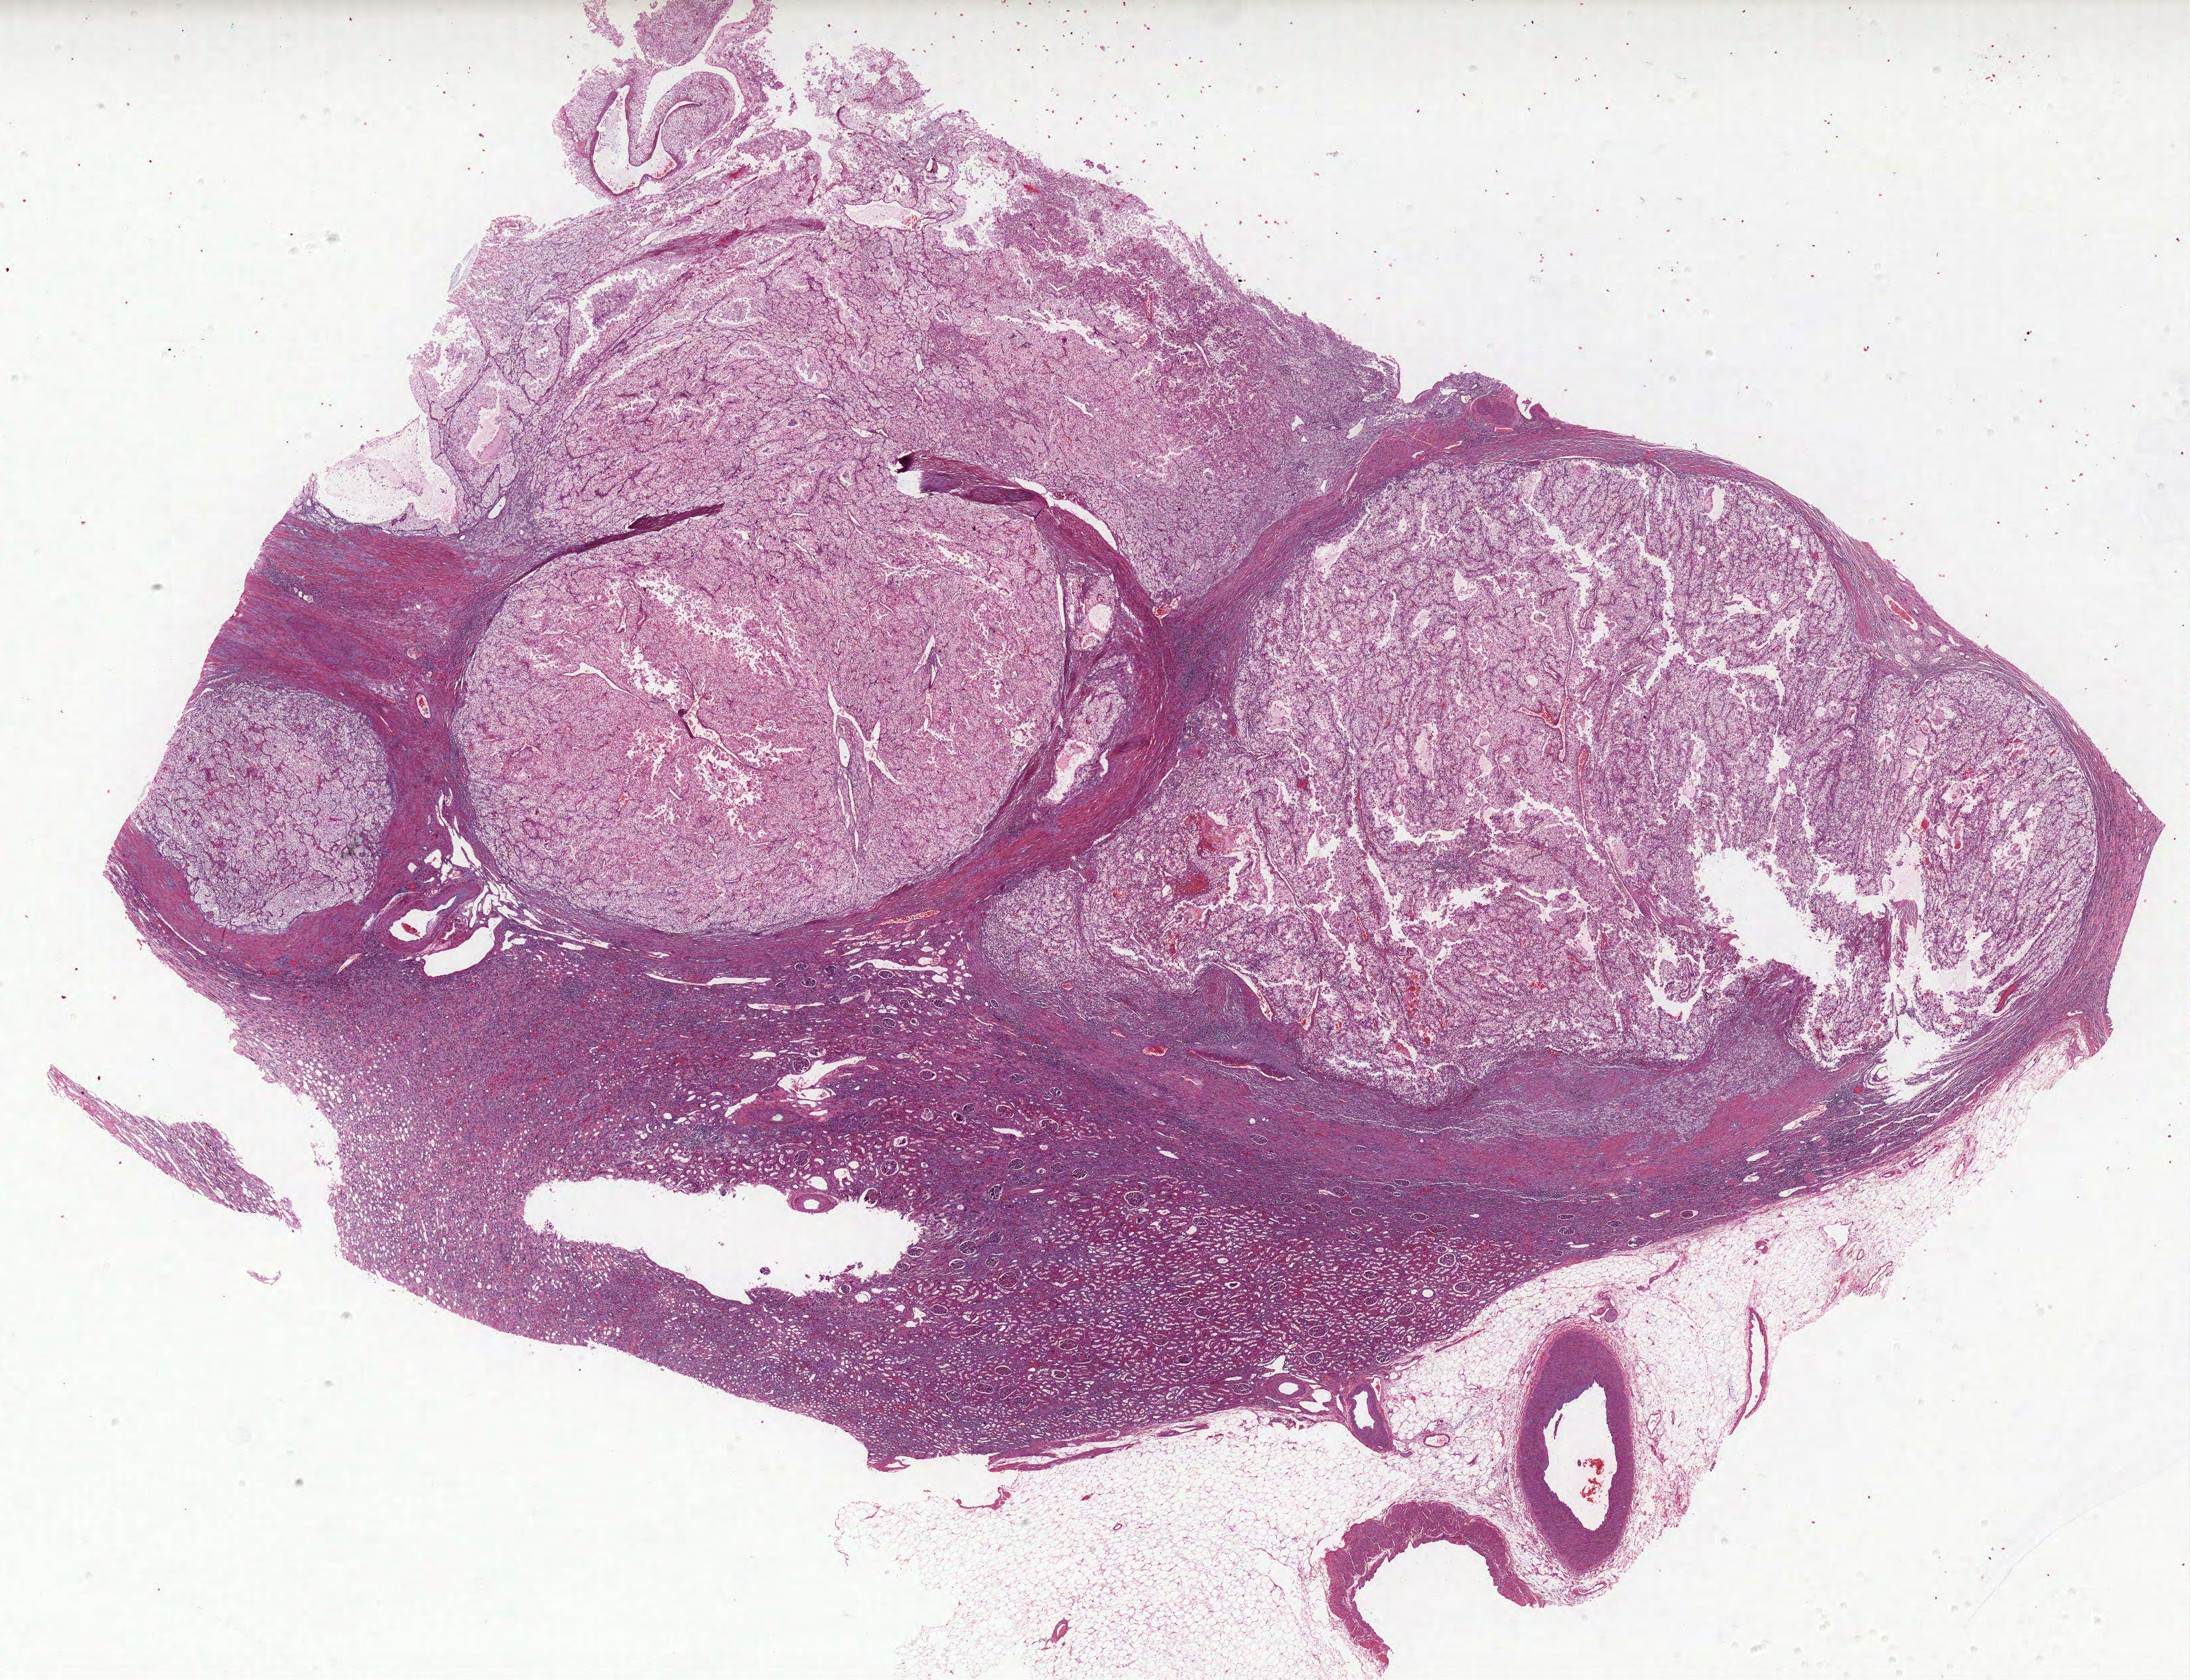
Digitized H&E-stained tissue section (whole slide), whole scanned area (about 26.1 x 20.1 mm, slide scanned at 40x) shown as a low-resolution overview; FFPE section; kidney, primary tumour sample. Female, age 59 years at initial diagnosis. Histologic grade: G4 (undifferentiated).
• TNM: T3a N0 M1
• AJCC pathologic stage: IV
• pathologic diagnosis: Clear cell adenocarcinoma, NOS